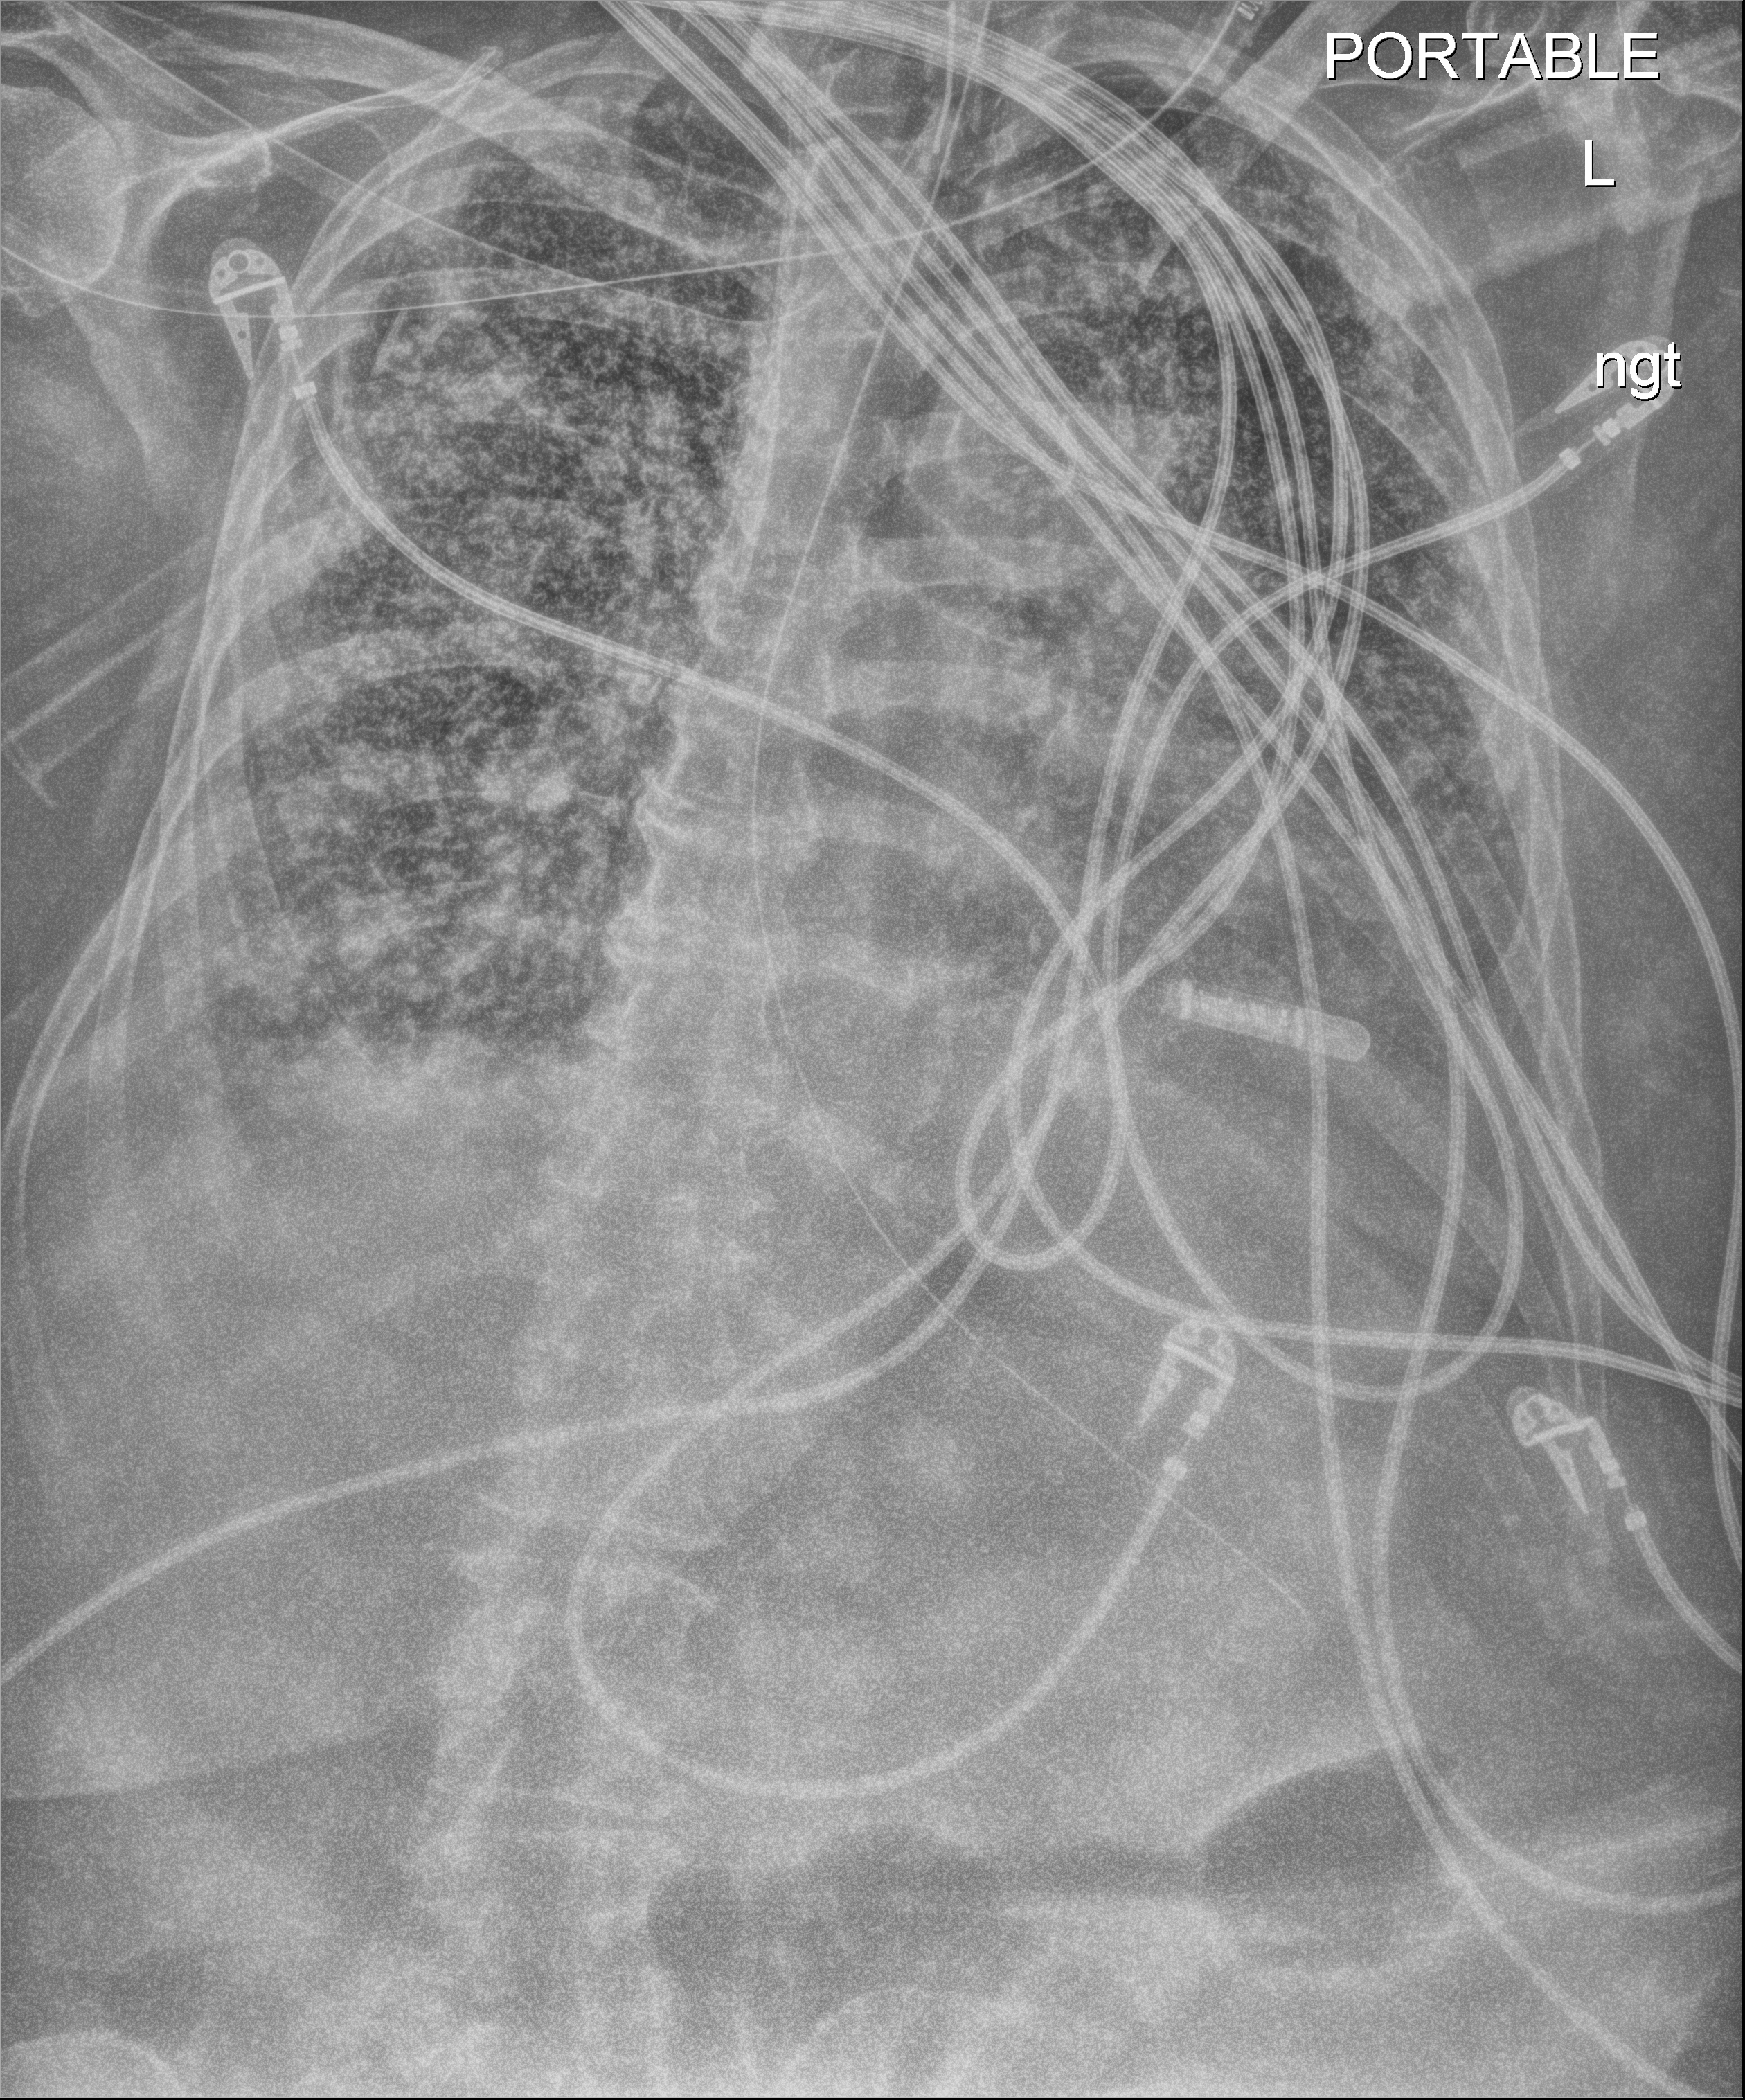
Chest X-ray (portable), anteroposterior (AP) projection. Patient hospitalised with COVID-19; female, aged 60–74 years.
Admission-level facts for this patient (not findings on this image; timing relative to this image not recorded): smoking status (admission record): former; admitted to intensive care during this hospital stay: yes.